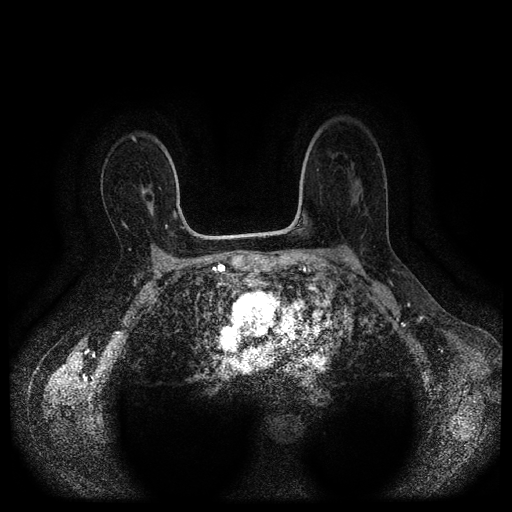
Breast MRI (dynamic contrast-enhanced, multi-phase), one axial slice. Dynamic contrast-enhanced series, time point 2 of 5 at this slice position (early post-contrast). 1.5 T. TE 2.6 ms, TR 5.4 ms. 512 × 512 image matrix, field of view 340 × 340 mm. Patient: female, 53 years.
Outlined on this slice (semi-automatic segmentation, software-assisted and operator-edited):
- breast lesion (labelled 'tumour' in the annotation; benign lesions carry a separate 'benign' label): box from (x=140, y=183) to (x=154, y=217) px